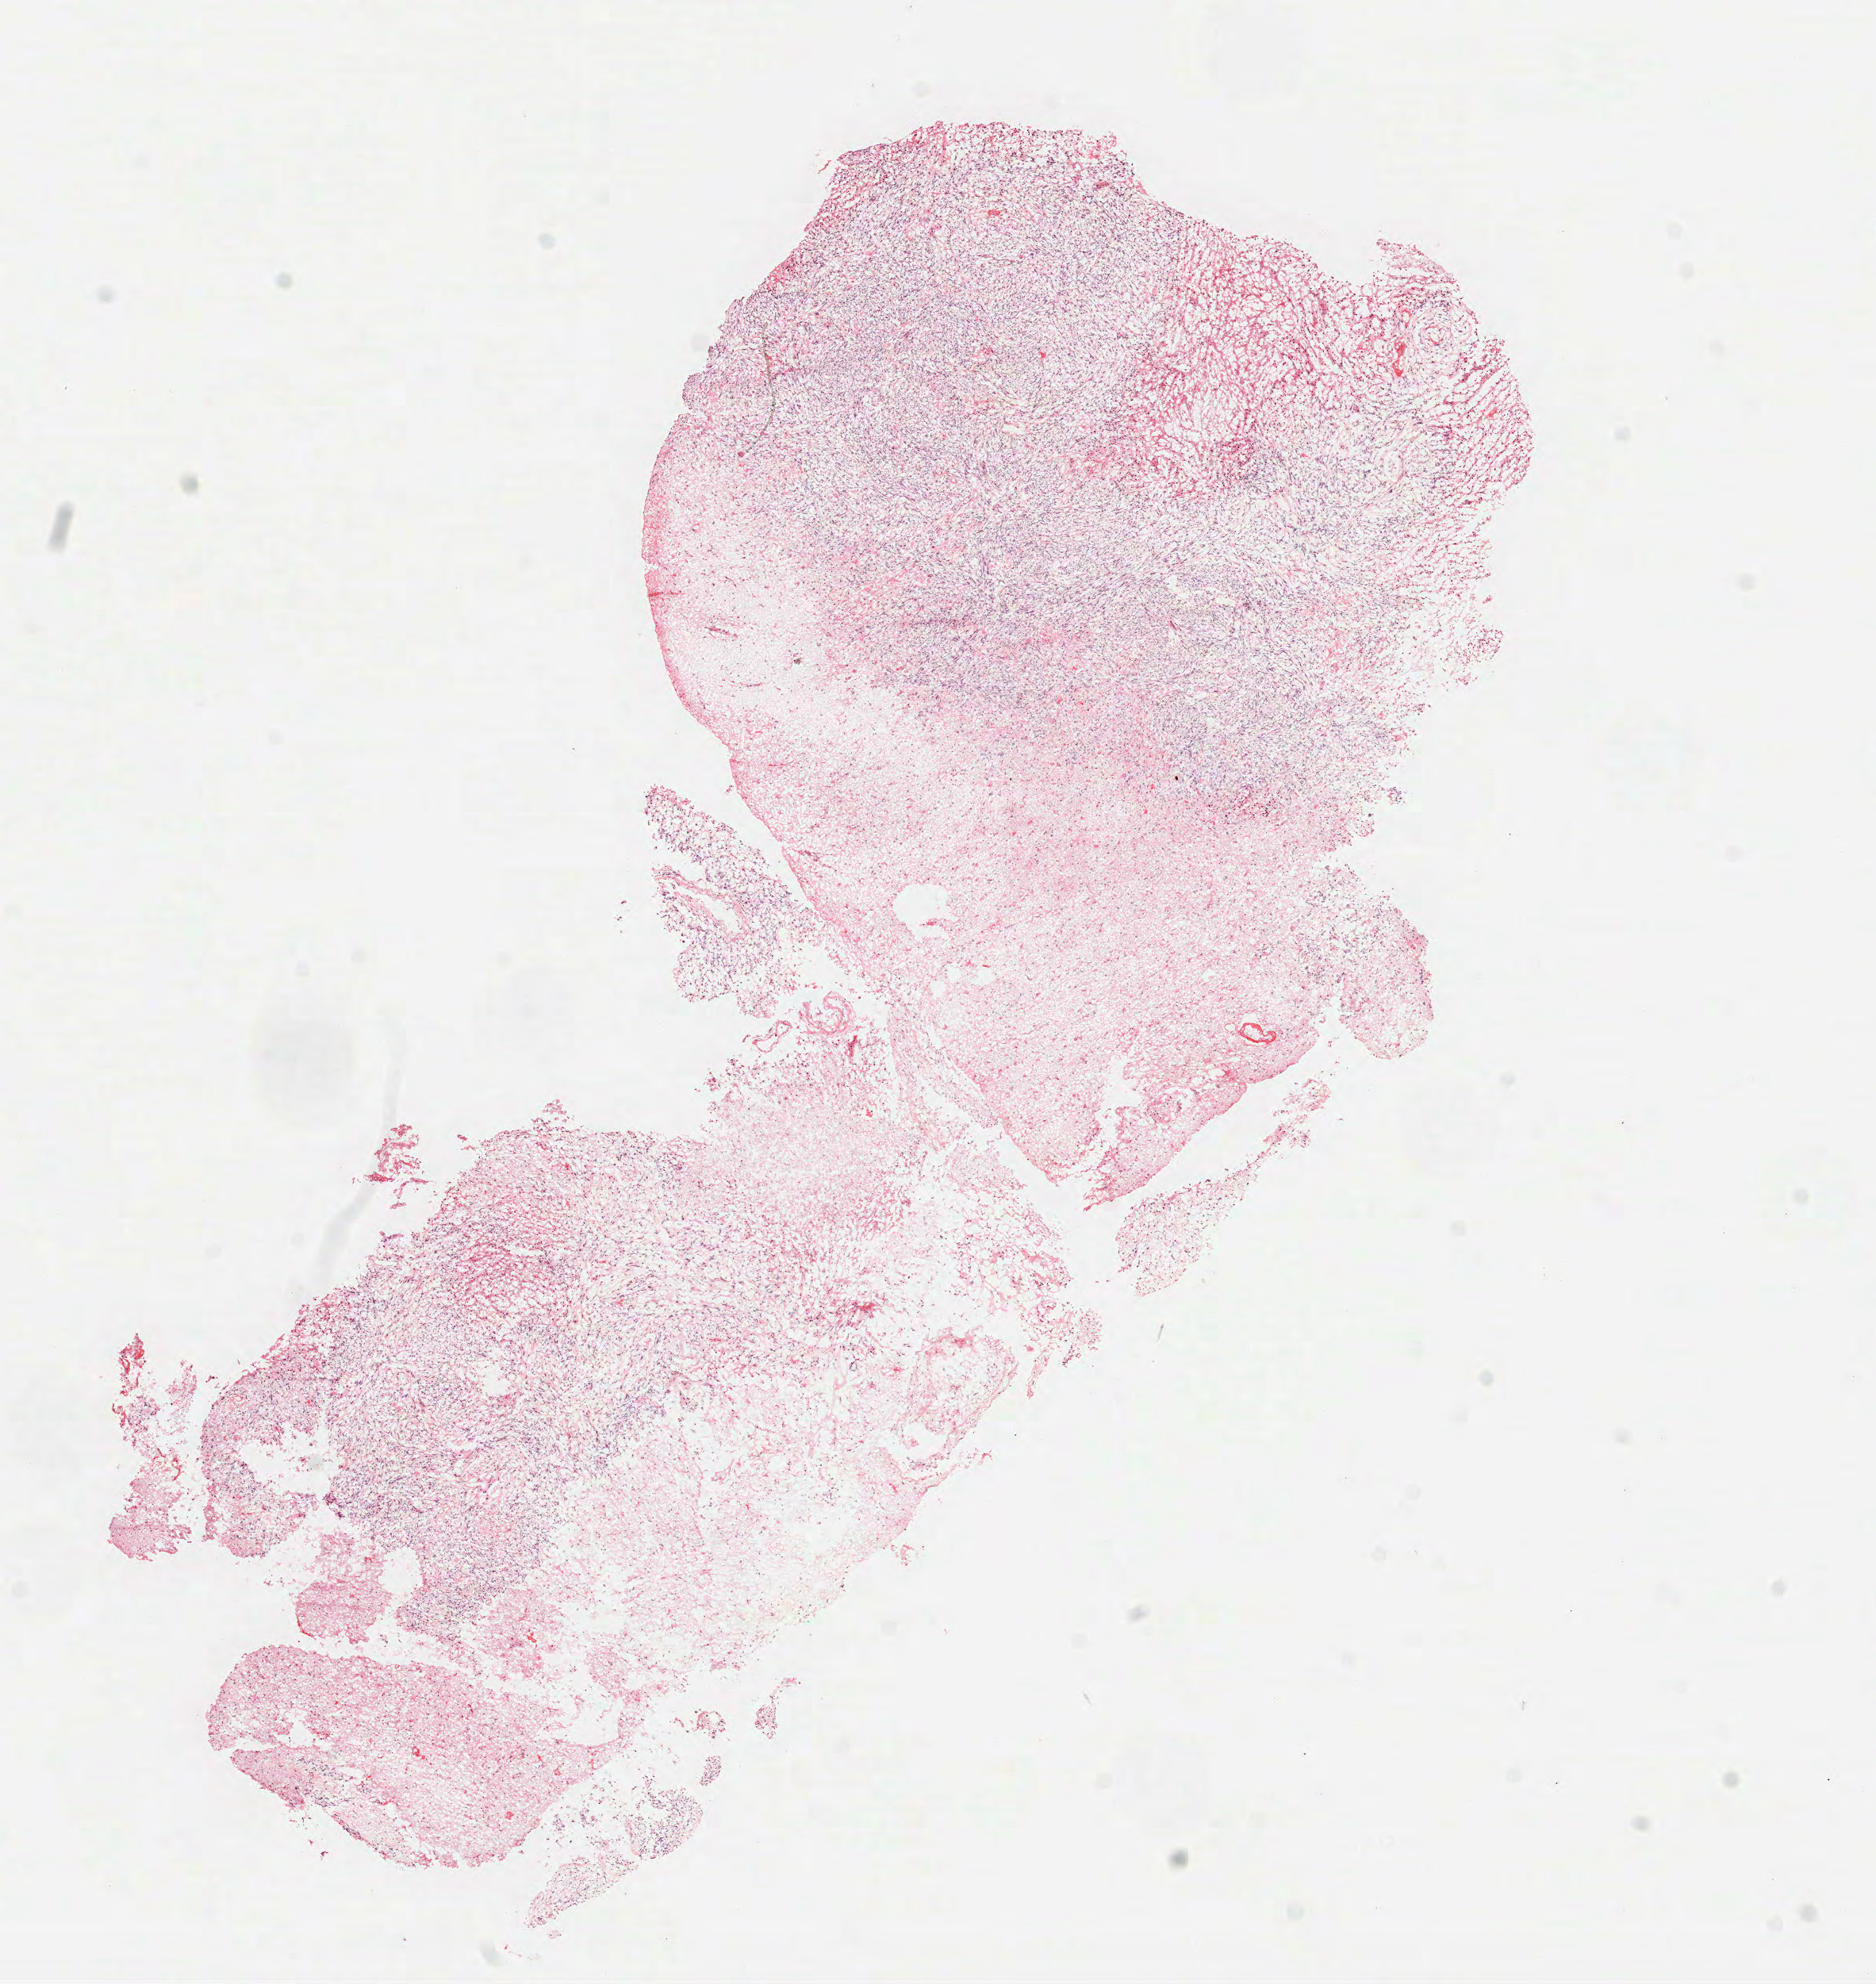
Hematoxylin and eosin (H&E) stained whole-slide image, whole scanned area (about 9.5 x 10.1 mm) shown as a low-resolution overview. Frozen section. Brain, recurrent tumour sample. Male, age 36 years at initial diagnosis. Pathologist review of this section (percent, as recorded): tumour cells 90%, tumour nuclei 75%, normal cells 0%, stromal cells 0%, necrosis 10%.
• this section: recurrent tumour
• patient diagnosis: Glioblastoma